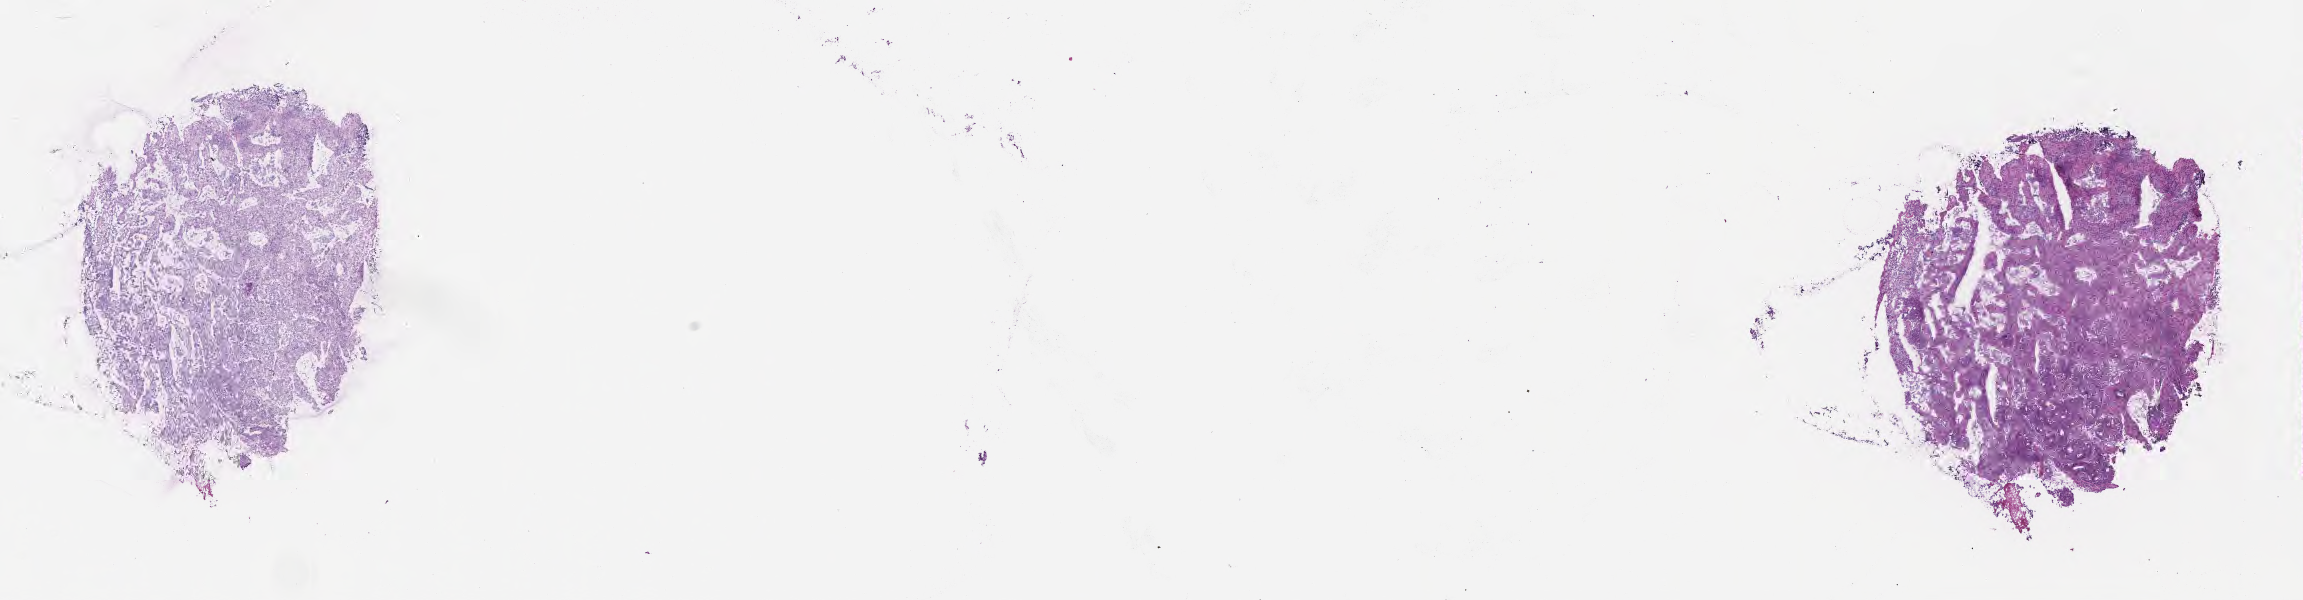
Digitized hematoxylin and eosin (H&E)-stained section — shown as a low-resolution overview of the whole scanned area (about 18.6 x 4.9 mm), frozen section, primary tumor, site: sigmoid colon. Male patient; age at initial diagnosis 75 years. Tumor grade: G2 (moderately differentiated). Slide review estimates, as recorded: tumor cells 85%, tumor nuclei 85%, stromal cells 15%, necrosis 0%, normal cells 0%. Inflammatory infiltration, as recorded: lymphocyte infiltration 4%, monocyte infiltration 2%, neutrophil infiltration 6%.
* section: bottom of the tissue portion
* histologic diagnosis: Adenocarcinoma, NOS
* AJCC pathologic stage: Stage IIIA